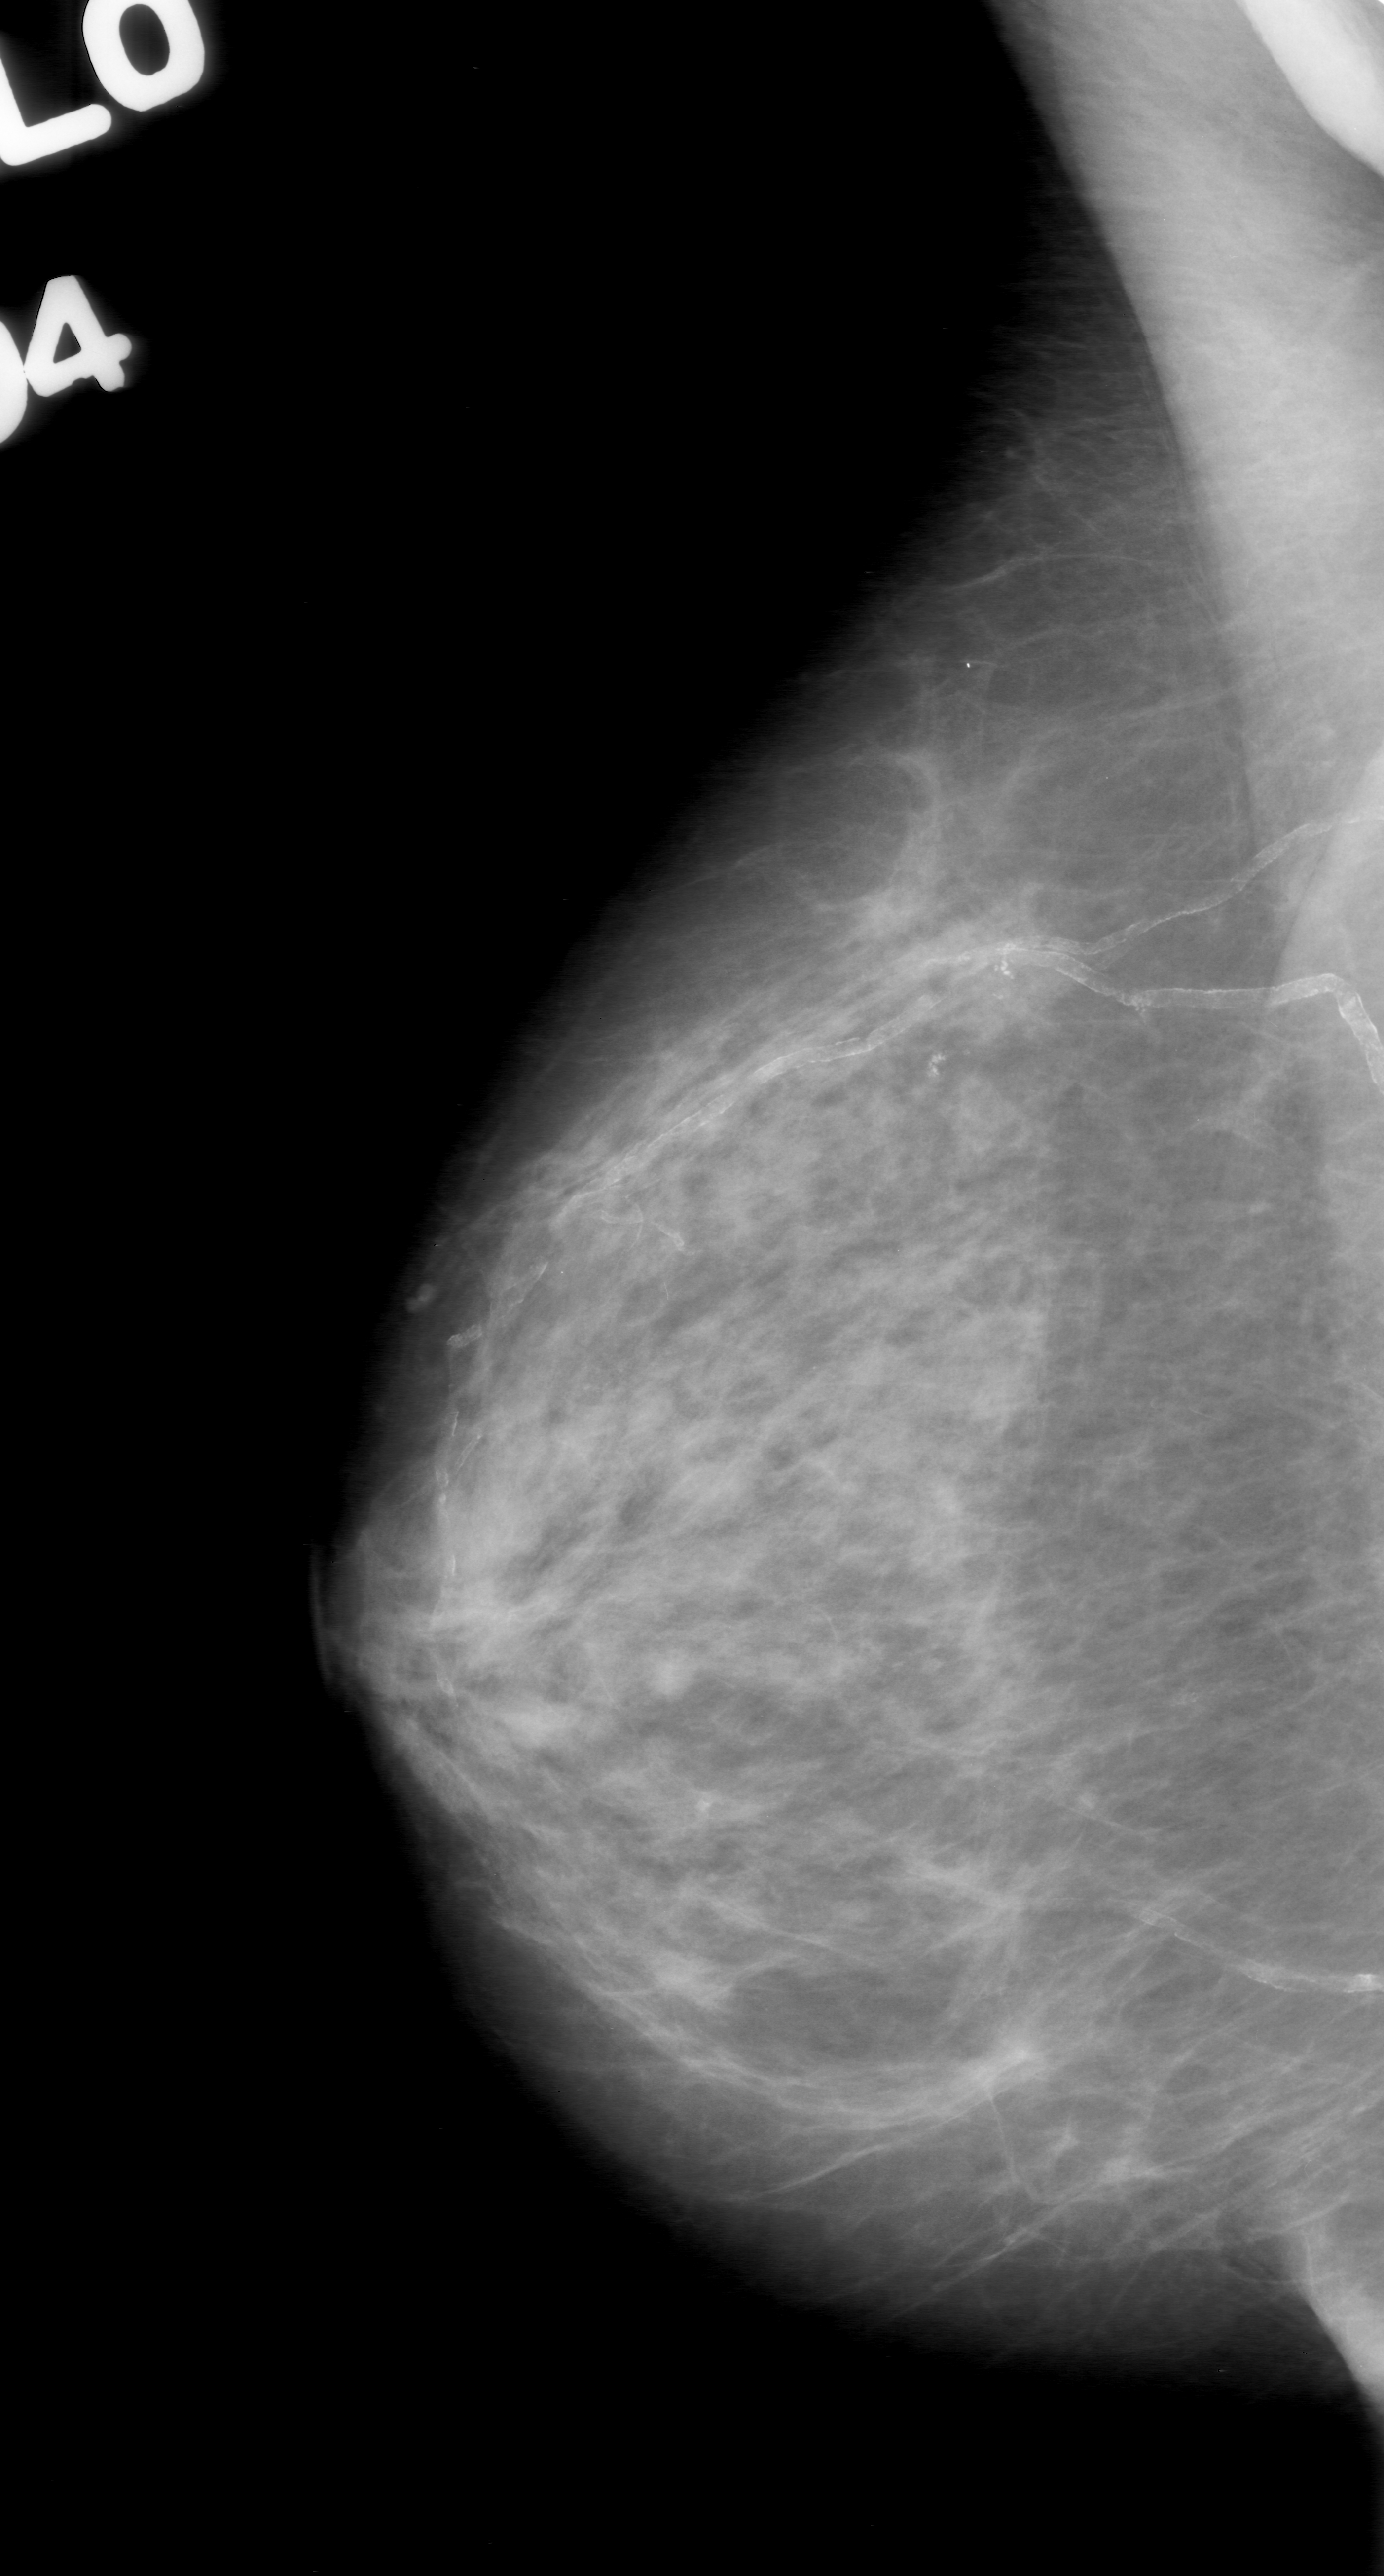
Mammogram (digitized film); right breast; mediolateral oblique (MLO) view; 1384 × 2576 image matrix.
Marked abnormalities (boxes around the expert regions of interest):
- calcifications, morphology coarse, distribution clustered; BI-RADS assessment category 0 (incomplete: needs additional imaging); subtlety rating 5 on a 1 (subtle) to 5 (obvious) scale; pathology (as recorded): benign: box from (x=892, y=876) to (x=1099, y=1073) px